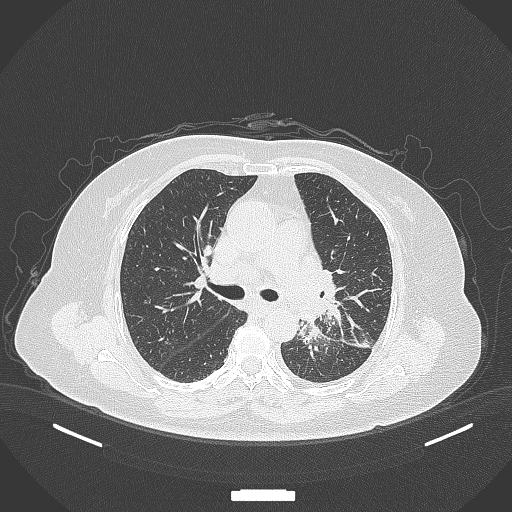
Chest CT, one axial slice; slice 218 of 322 in the series (ordered by position); reconstruction kernel B70f; 120 kVp; lung window (W 1500 / L -600 HU); 512 × 512 image matrix, field of view 400 × 400 mm. Patient: female, 69 years. Case-level facts recorded for this patient, not image findings: clinical TNM (as recorded): T2b N3 M1.
Structures marked on this image (bounding box drawn by a radiologist):
- lung tumour (recorded histology: adenocarcinoma): bounding box <294,318,322,350> (left, top, right, bottom; pixels)